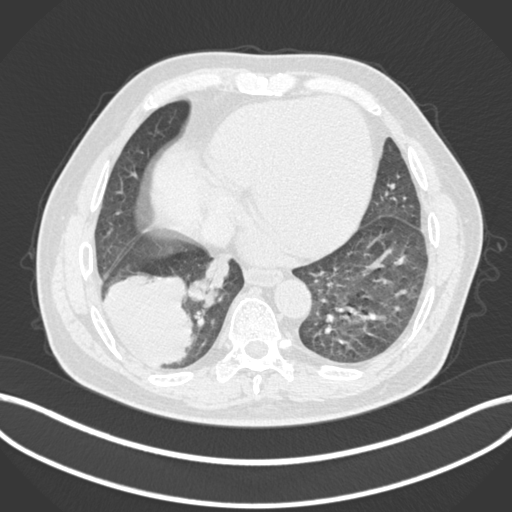
Chest CT, one axial slice. Slice 45 of 200 in the series (ordered by position). 120 kVp. Lung window (W 1500 / L -600 HU). 1 mm slice thickness. 512 × 512 image matrix, field of view 400 × 400 mm. Male patient, age 59 years.
Structures marked on this image (bounding box drawn by a radiologist):
- lung tumour (recorded histology: adenocarcinoma): bounding box (x1, y1, x2, y2) in pixels: (100, 271, 193, 368)